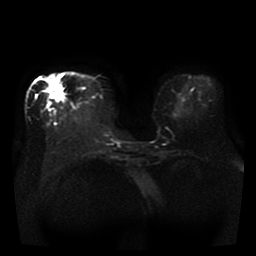
Breast MRI, one axial slice; position 12 of 41 along the scan axis; diffusion-weighted series; image 2 of 4 stored at this slice position (different b-values; order by instance number); 1.5 T; 5 mm slice thickness; 256 × 256 image matrix. Female patient.
Outlined on this slice (expert manual segmentation):
- tumour on diffusion-weighted imaging: bounding box (x1, y1, x2, y2) in pixels: (49, 85, 63, 101)